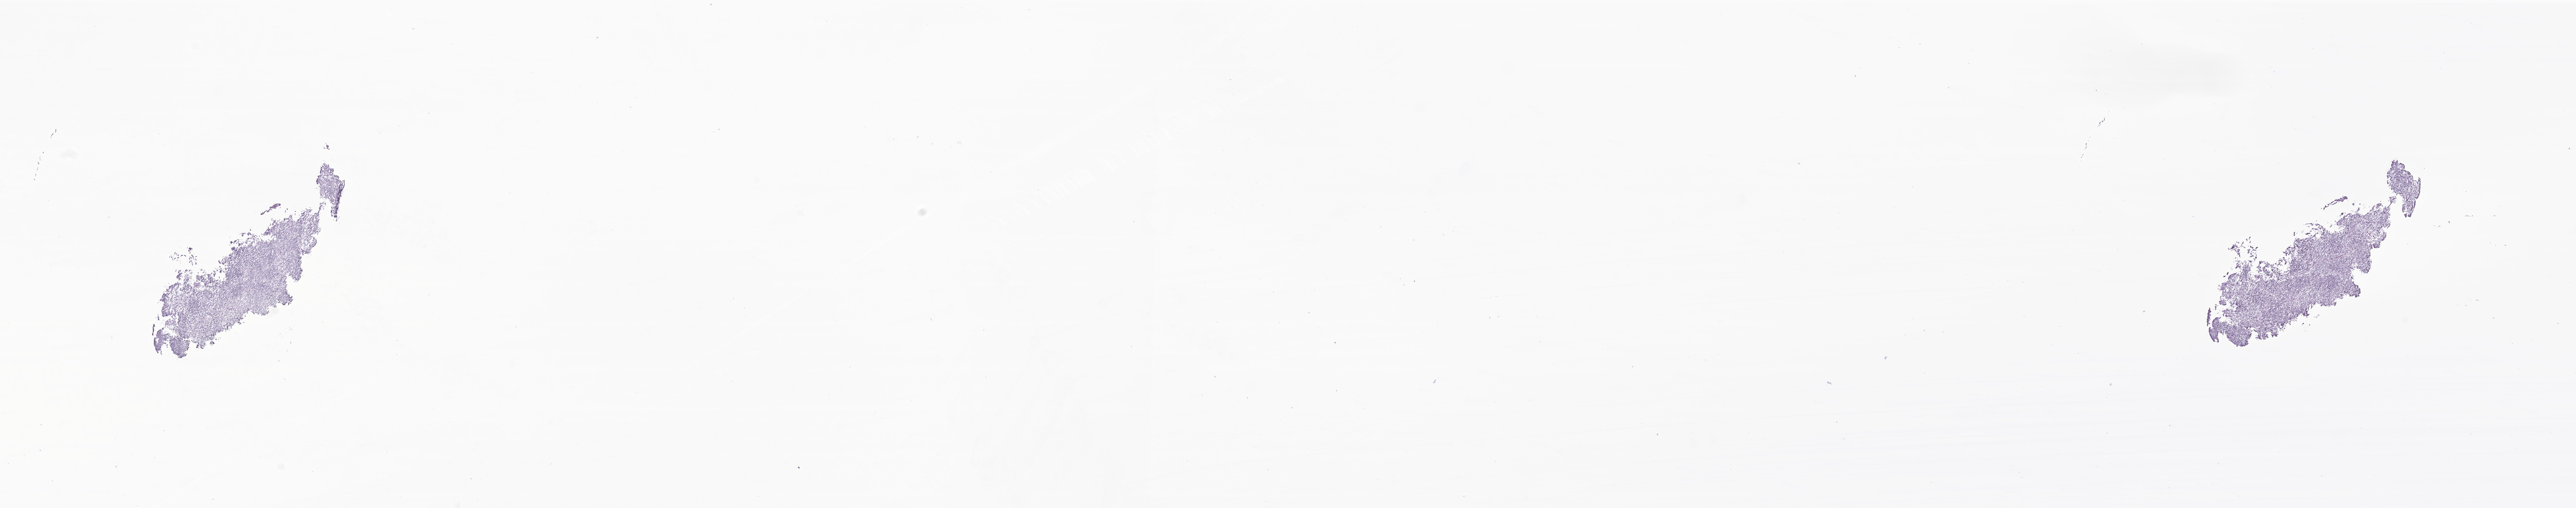
H&E whole-slide image of tumor tissue from the brain, whole scanned area (about 31.7 x 6.3 mm) shown as a low-resolution overview, frozen section. Patient male; age 191 months (15 years 11 months).
Recorded diagnosis: Medulloblastoma, NOS.